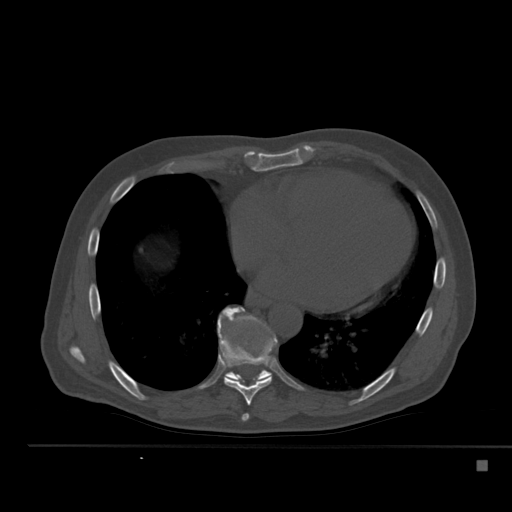
CT including the spine, one axial slice. Position 302 of 517 along the scan axis. Reconstruction kernel Br40s. 120 kVp. Bone window (W 1800 / L 400 HU). 1.5 mm slice thickness. 512 × 512 image matrix, field of view 408 × 408 mm. Patient: male, 70 years. Case-level facts recorded for this patient, not image findings: primary cancer: renal.
Annotated regions visible in this slice (semi-automatically segmented with operator editing):
- T7 vertebra: bounding box [x1, y1, x2, y2] px = [242, 413, 250, 421]
- T8 vertebra: [217, 307, 278, 405]
- T9 vertebra: [223, 307, 272, 383]